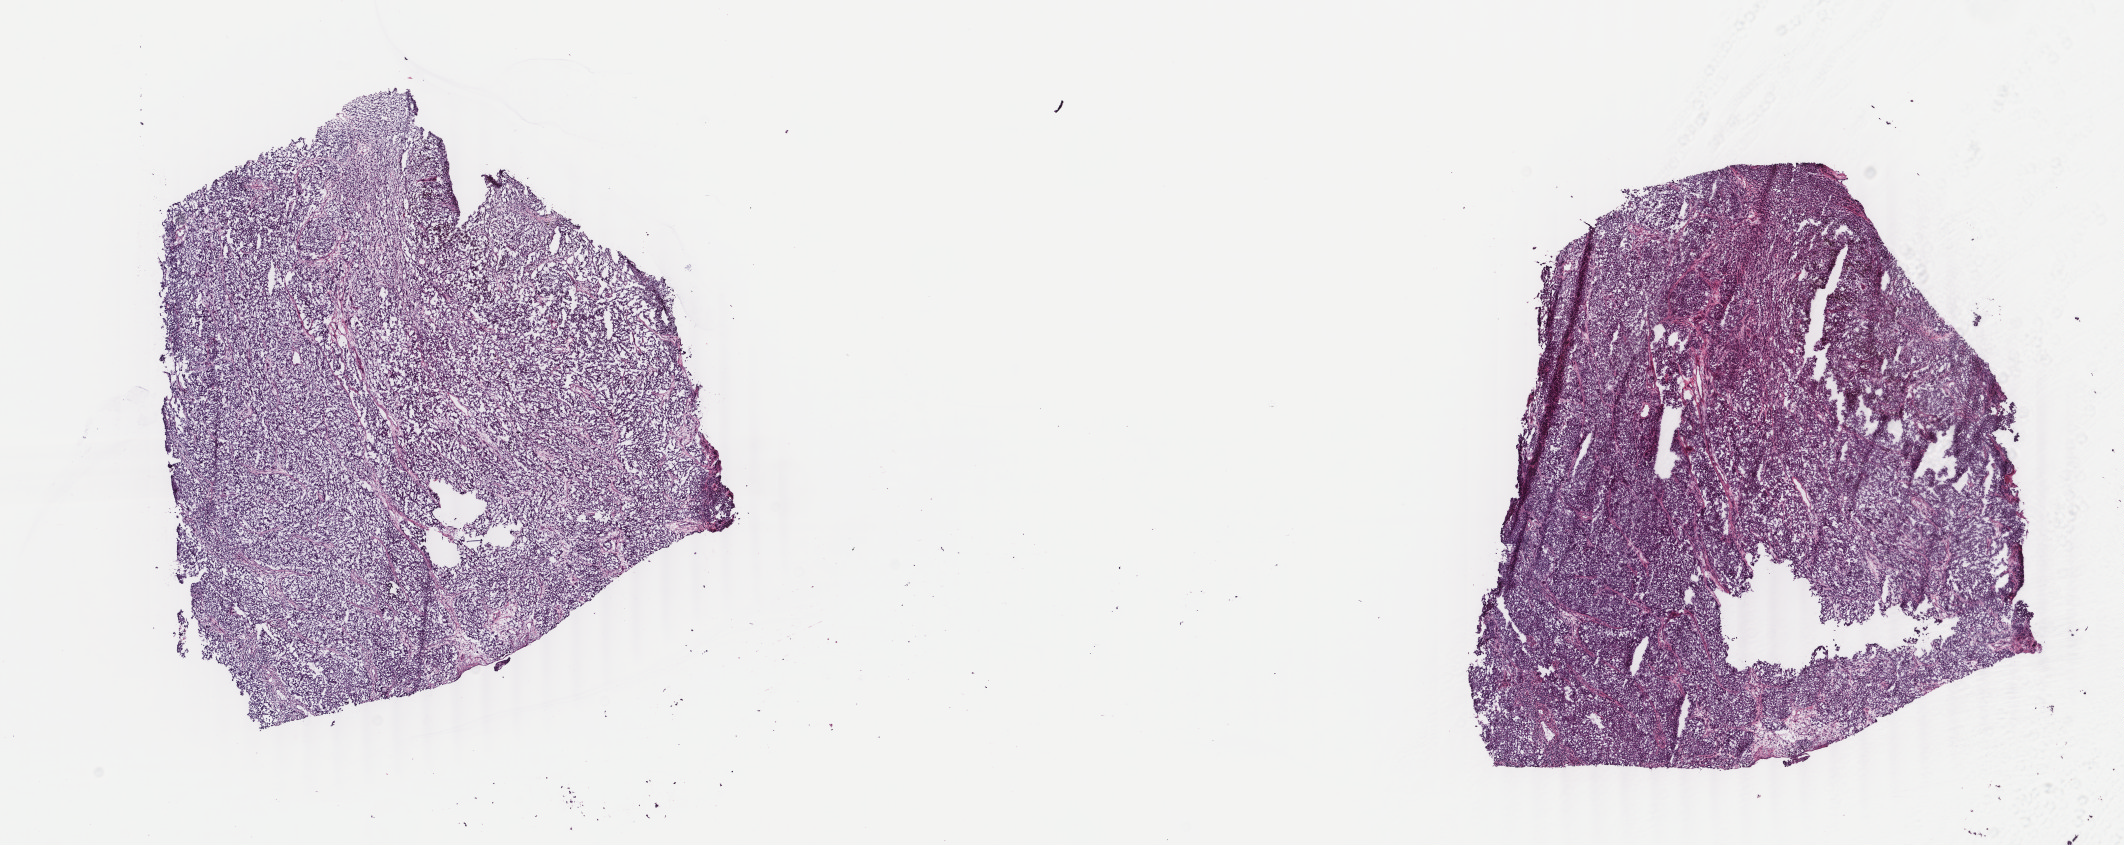
Digitized Hematoxylin and eosin (H&E) stained tissue section (whole slide) — whole scanned area (about 16.9 x 6.7 mm, slide scanned at 40x) shown as a low-resolution overview. Frozen section from the top of the tissue portion. Sample: primary tumour, skin. Female, age 71 years at initial diagnosis. Composition of this section per pathologist review: tumour cells 100%, tumour nuclei 95%, normal cells 0%, stromal cells 0%, necrosis 0%. Inflammatory infiltration, as recorded: lymphocyte infiltration 0%, monocyte infiltration 0%, neutrophil infiltration 0%.
• AJCC pathologic stage: IIB (7th edition)
• histologic diagnosis: Malignant melanoma, NOS